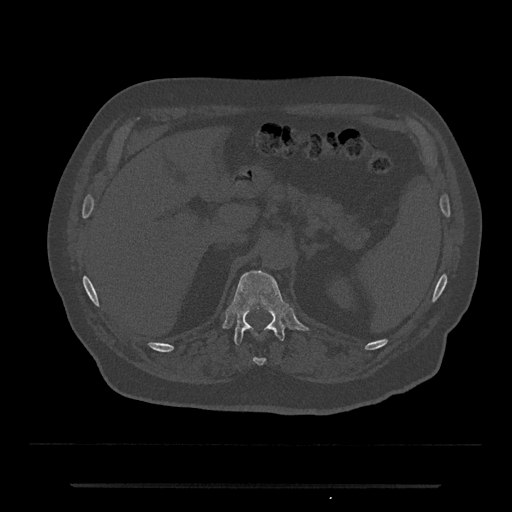
CT including the spine, one axial slice; bone window (W 1800 / L 400 HU); 512 × 512 image matrix. Male patient, age 80 years. Case-level facts recorded for this patient, not image findings: primary cancer: prostate; vertebrae with lytic lesions (as recorded): L1, T11.
Annotated regions visible in this slice (semi-automatically segmented with operator editing):
- T11 vertebra: bounding box <253,357,265,366> (left, top, right, bottom; pixels)
- T12 vertebra: <229,270,289,345>